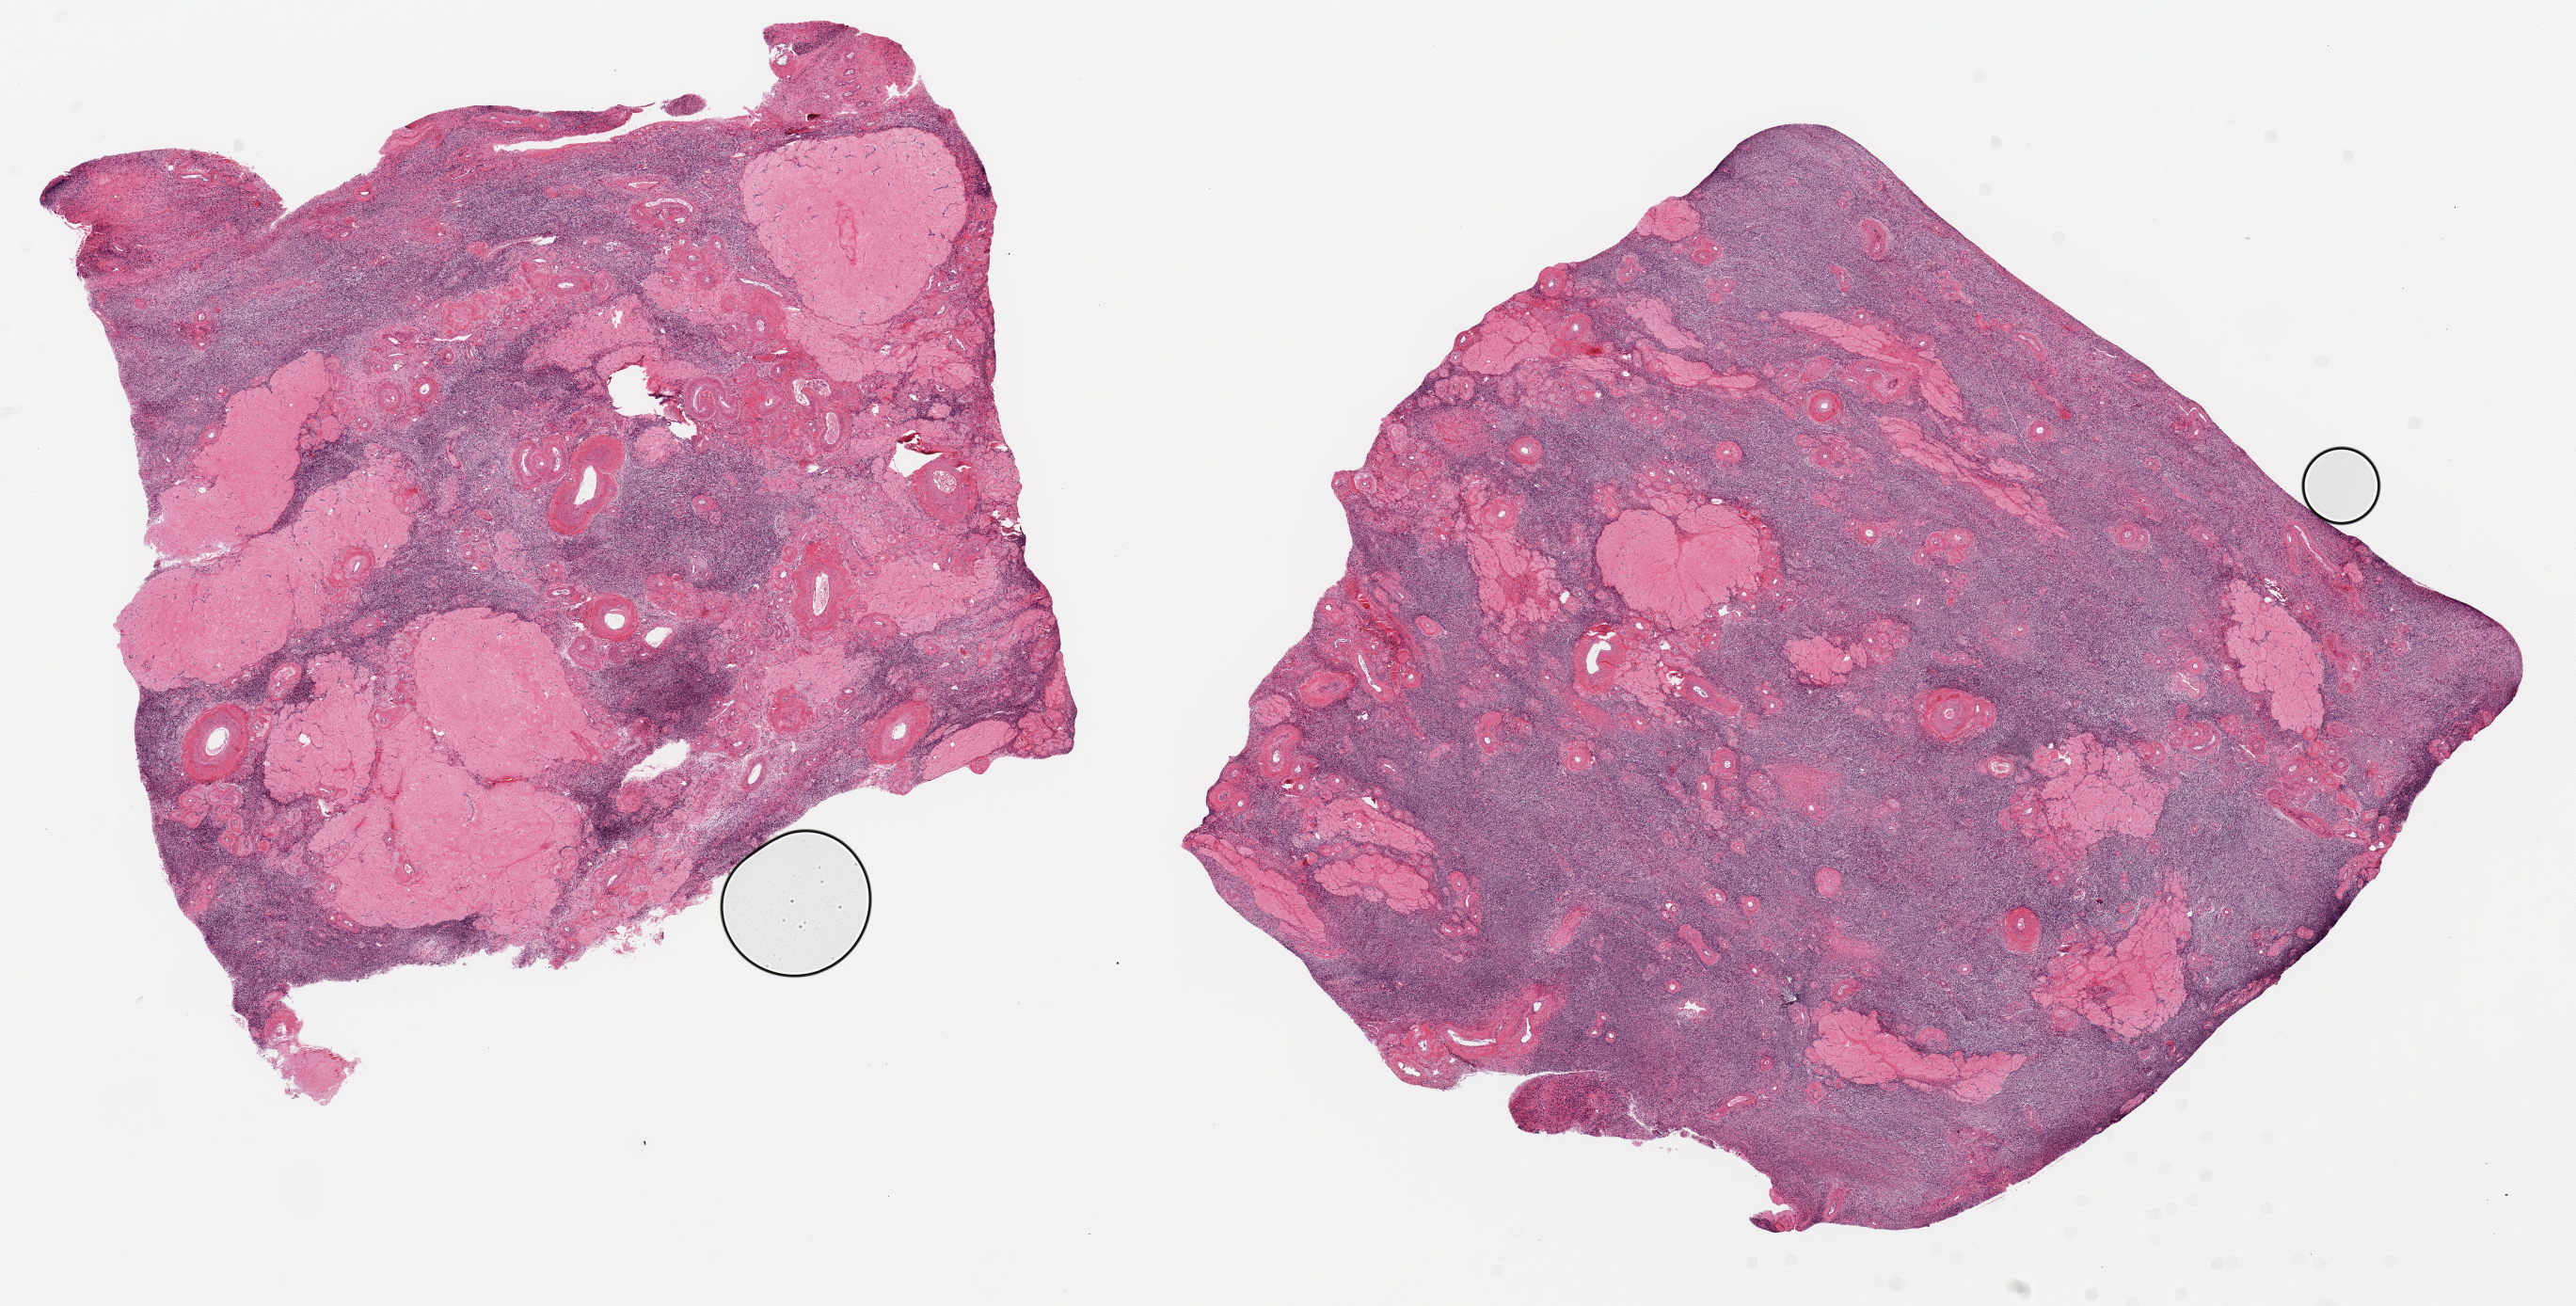
Digitized haematoxylin and eosin-stained section — whole scanned area (about 21.7 x 11.0 mm, acquisition: 20x scan) shown as a low-resolution overview. PAXgene-fixed, paraffin-embedded tissue. Sampled site (target tissue): ovary. Donor tissue sample. Donor: female.
Reviewer comment on this tissue sample: 2 pieces. 8x8 & 9x8mm; Atrophic. Numerous corpora albicans.